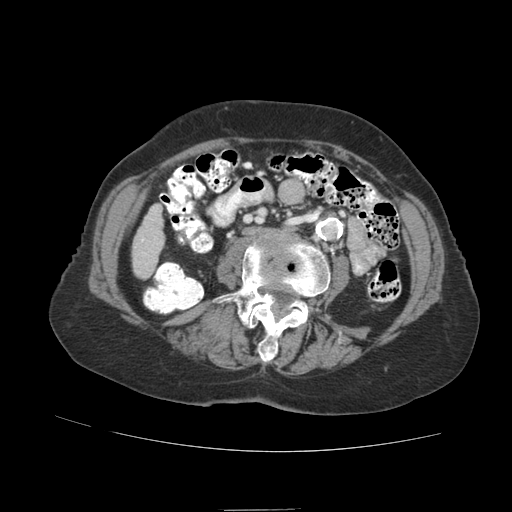
Contrast-enhanced abdominal CT (liver protocol), one axial slice. Position 12 of 89 along the scan axis. 140 kVp. Soft-tissue window (W 400 / L 40 HU). 512 × 512 image matrix. From the clinical record (not read from this slice): diagnosis: hepatocellular carcinoma (patient treated with transarterial chemoembolisation; whether this scan precedes or follows treatment is not stated here); TNM stage (as recorded): Stage-II; Child-Pugh class: A; tumour differentiation: moderately differentiated; tumour nodularity: multinodular.
Annotated regions visible in this slice (semi-automatically segmented with operator editing):
- liver parenchyma outside the tumour (the mass and vessels are separate outlines, so this box may not span the whole liver): bounding box [x1, y1, x2, y2] px = [132, 204, 164, 278]